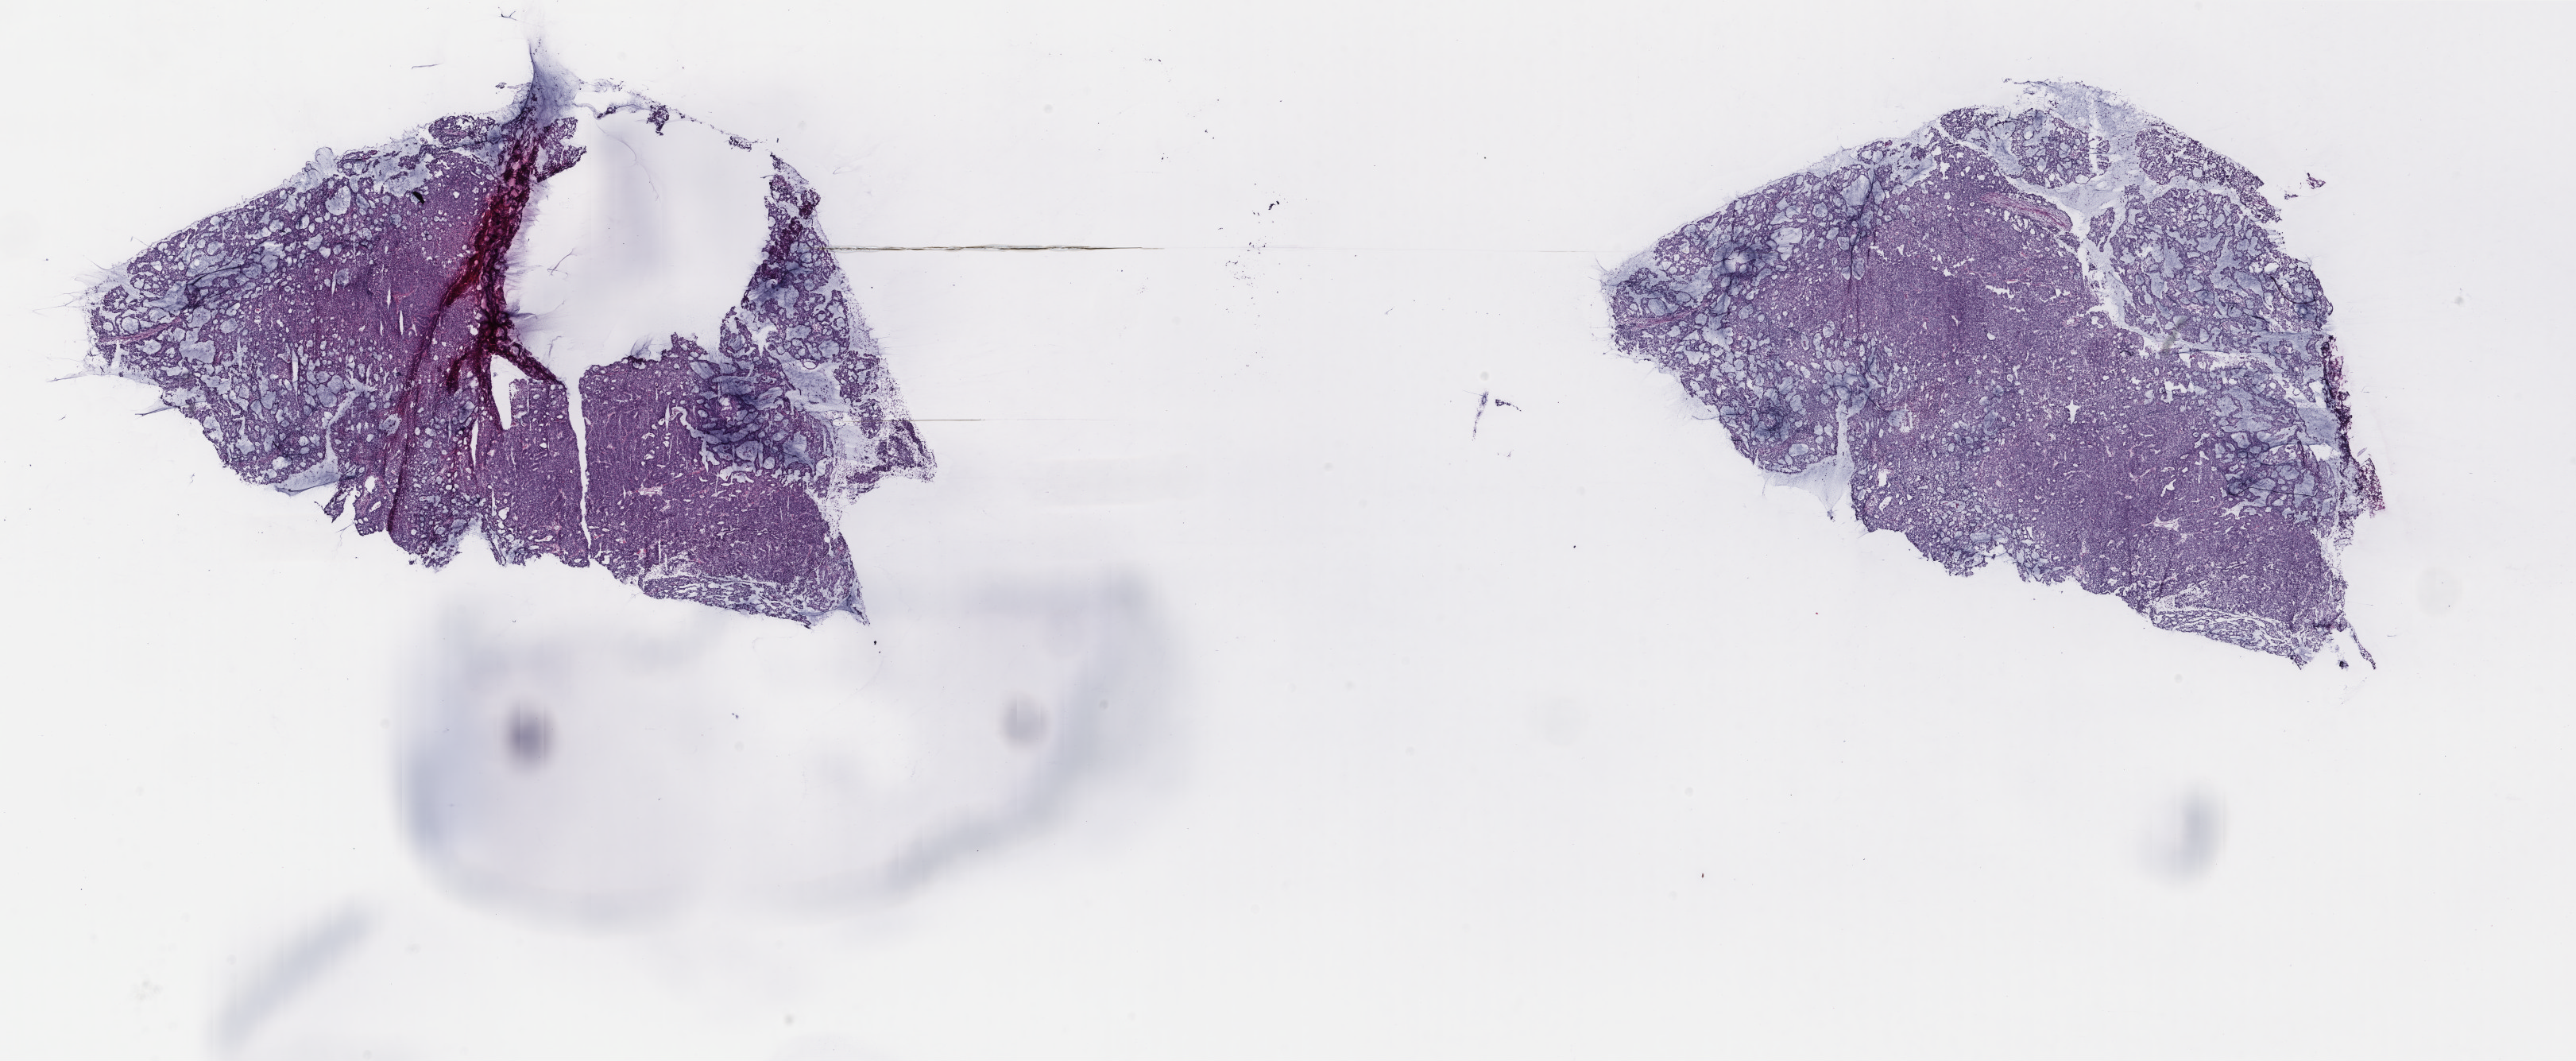
Digitized H&E-stained tissue section (whole slide), a low-resolution overview of the entire scanned area, about 25.7 x 10.6 mm, frozen section from the top of the tissue portion, uterus, primary tumour sample. Female patient; age at initial diagnosis 66 years. Histologic grade: G2 (moderately differentiated). Composition of this section per pathologist review: tumour cells 80%, tumour nuclei 80%, normal cells 0%, stromal cells 15%, necrosis 5%. Inflammatory infiltration, as recorded: lymphocyte infiltration 40%, monocyte infiltration 10%, neutrophil infiltration 40%.
- lymph nodes positive (case pathology): 0 of 11 examined
- FIGO stage: IB
- diagnosis: Endometrioid adenocarcinoma, NOS (endometrium)